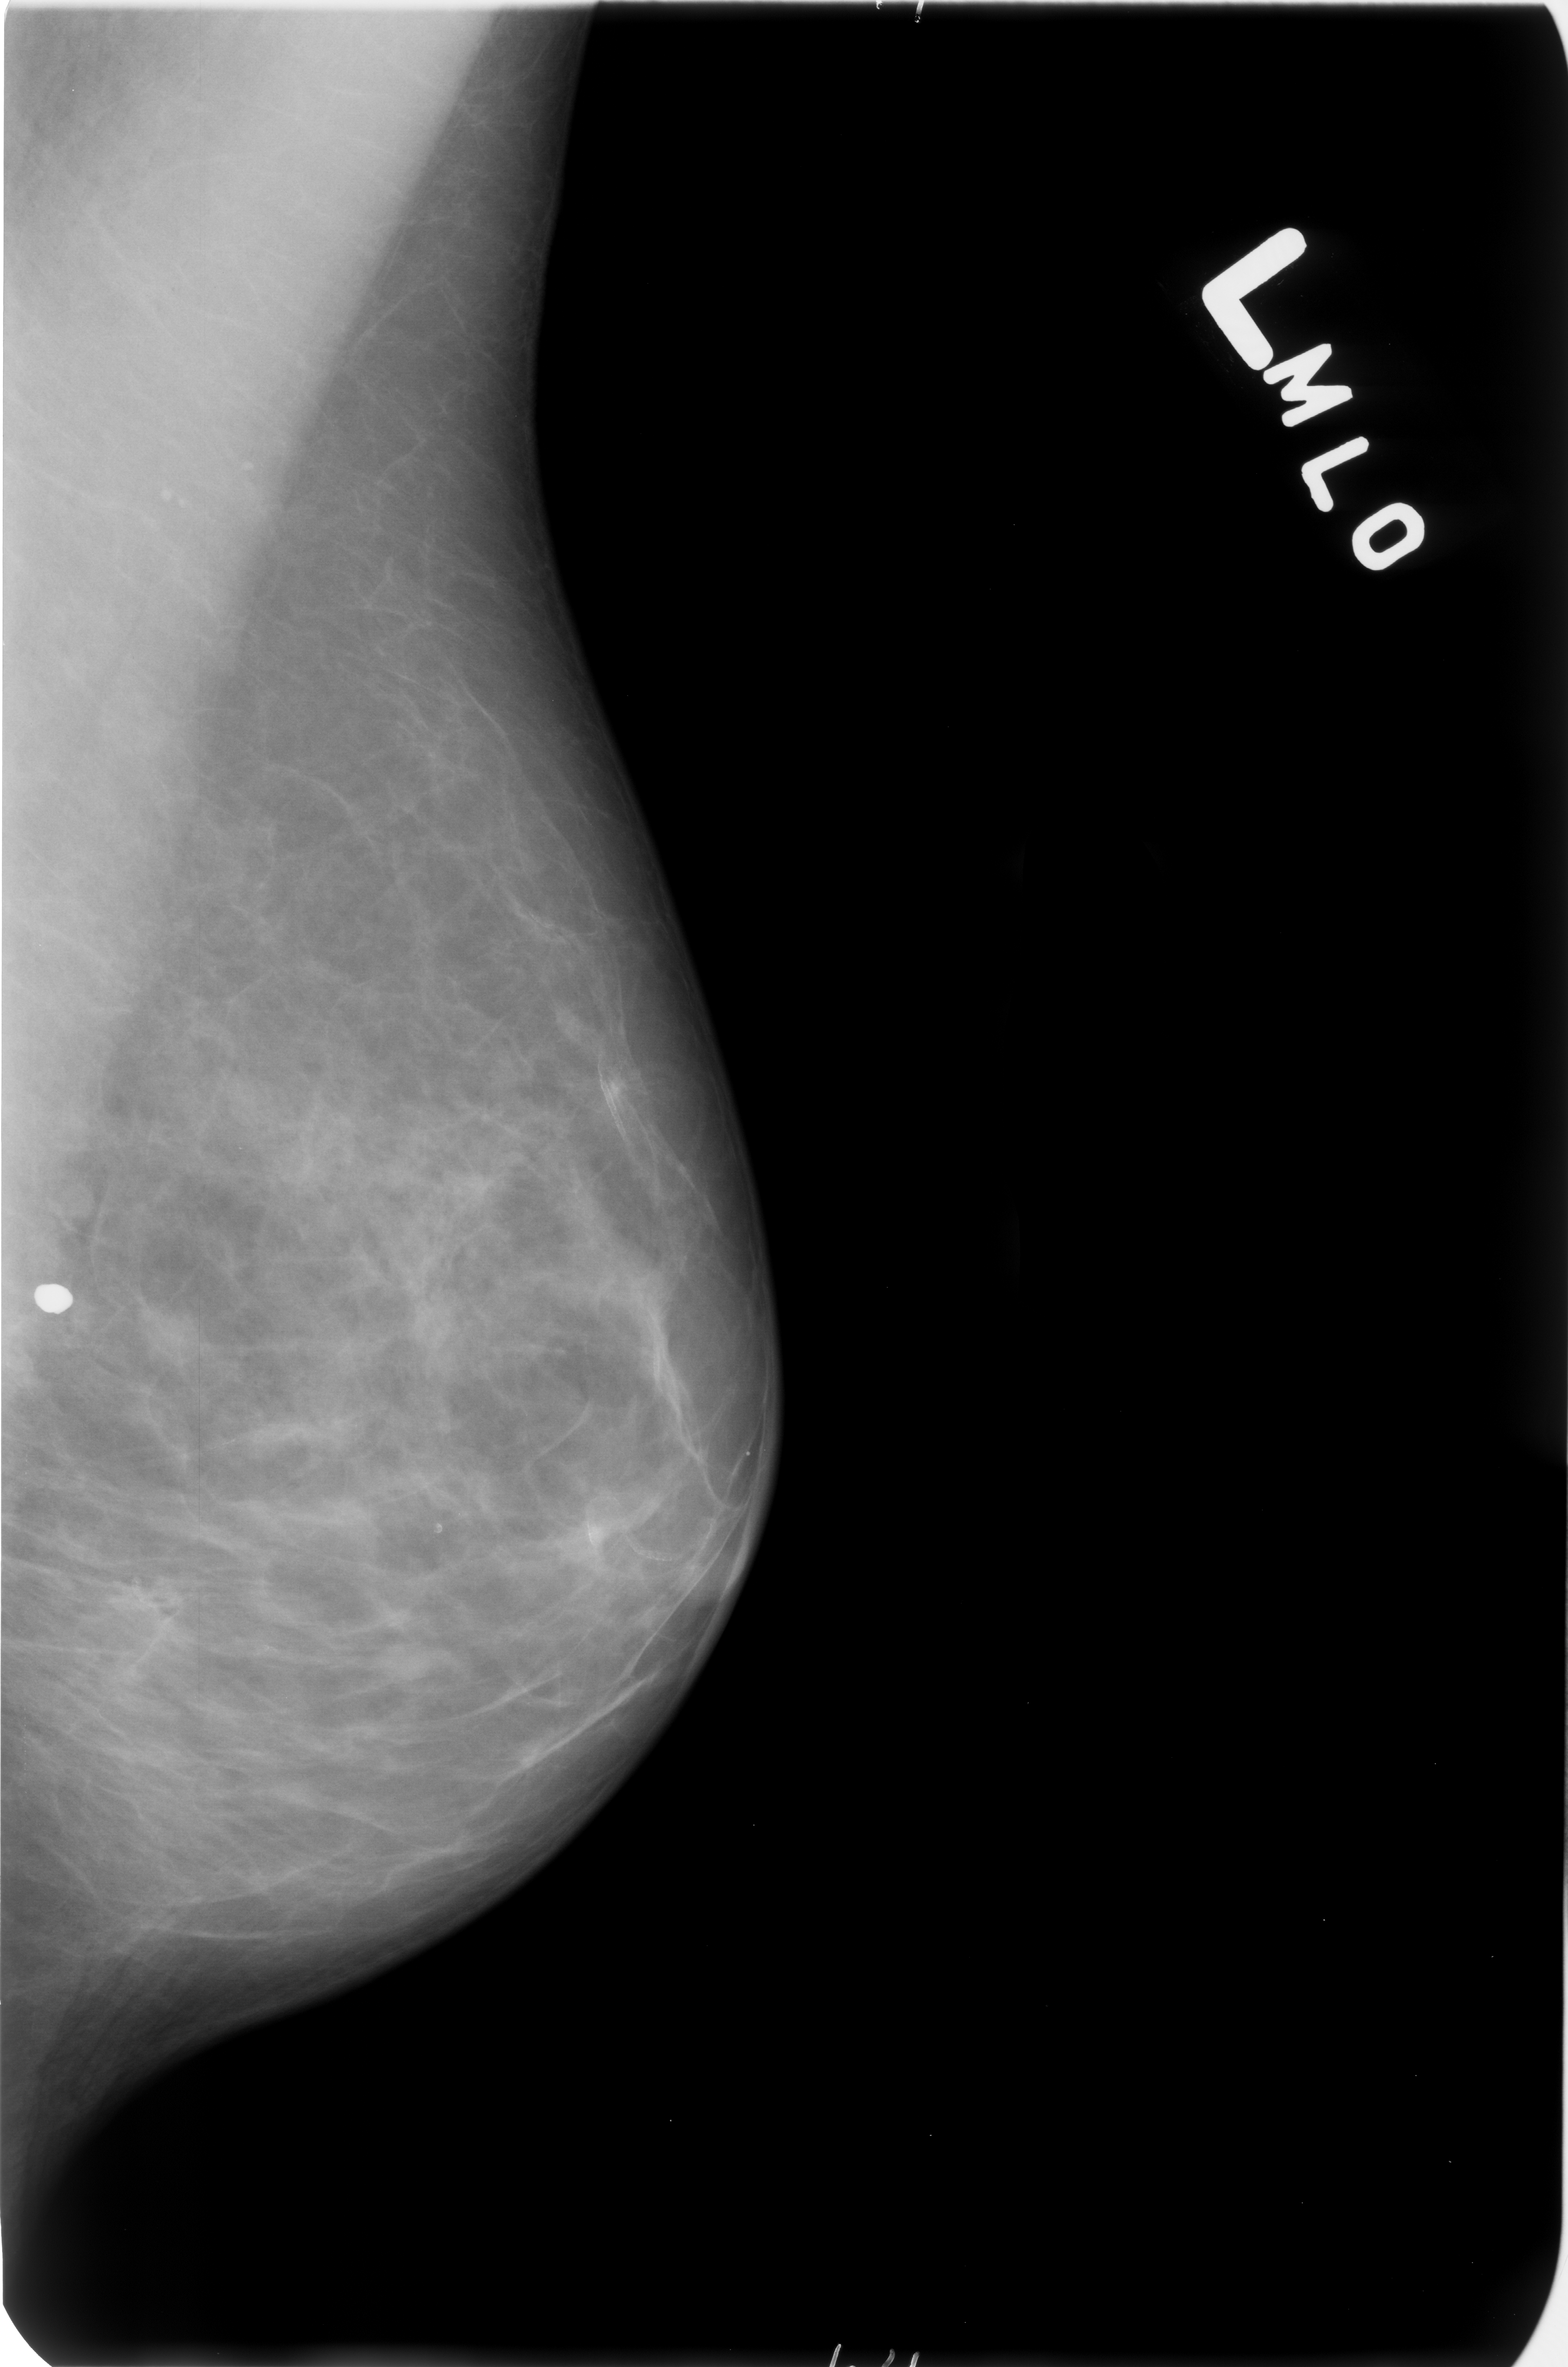
Scanned film-screen mammogram; left breast; MLO view; BI-RADS breast density category 2 (scale 1–4).
Radiologist-marked abnormalities on this image: Finding 1 of 2: calcifications, morphology coarse; BI-RADS assessment category 2; subtlety rating 5 on a 1 (subtle) to 5 (obvious) scale; benign without callback (not worked up further). Finding 2 of 2: calcifications, morphology vascular; BI-RADS assessment category 2; subtlety rating 5 on a 1 (subtle) to 5 (obvious) scale; benign without callback (not worked up further).